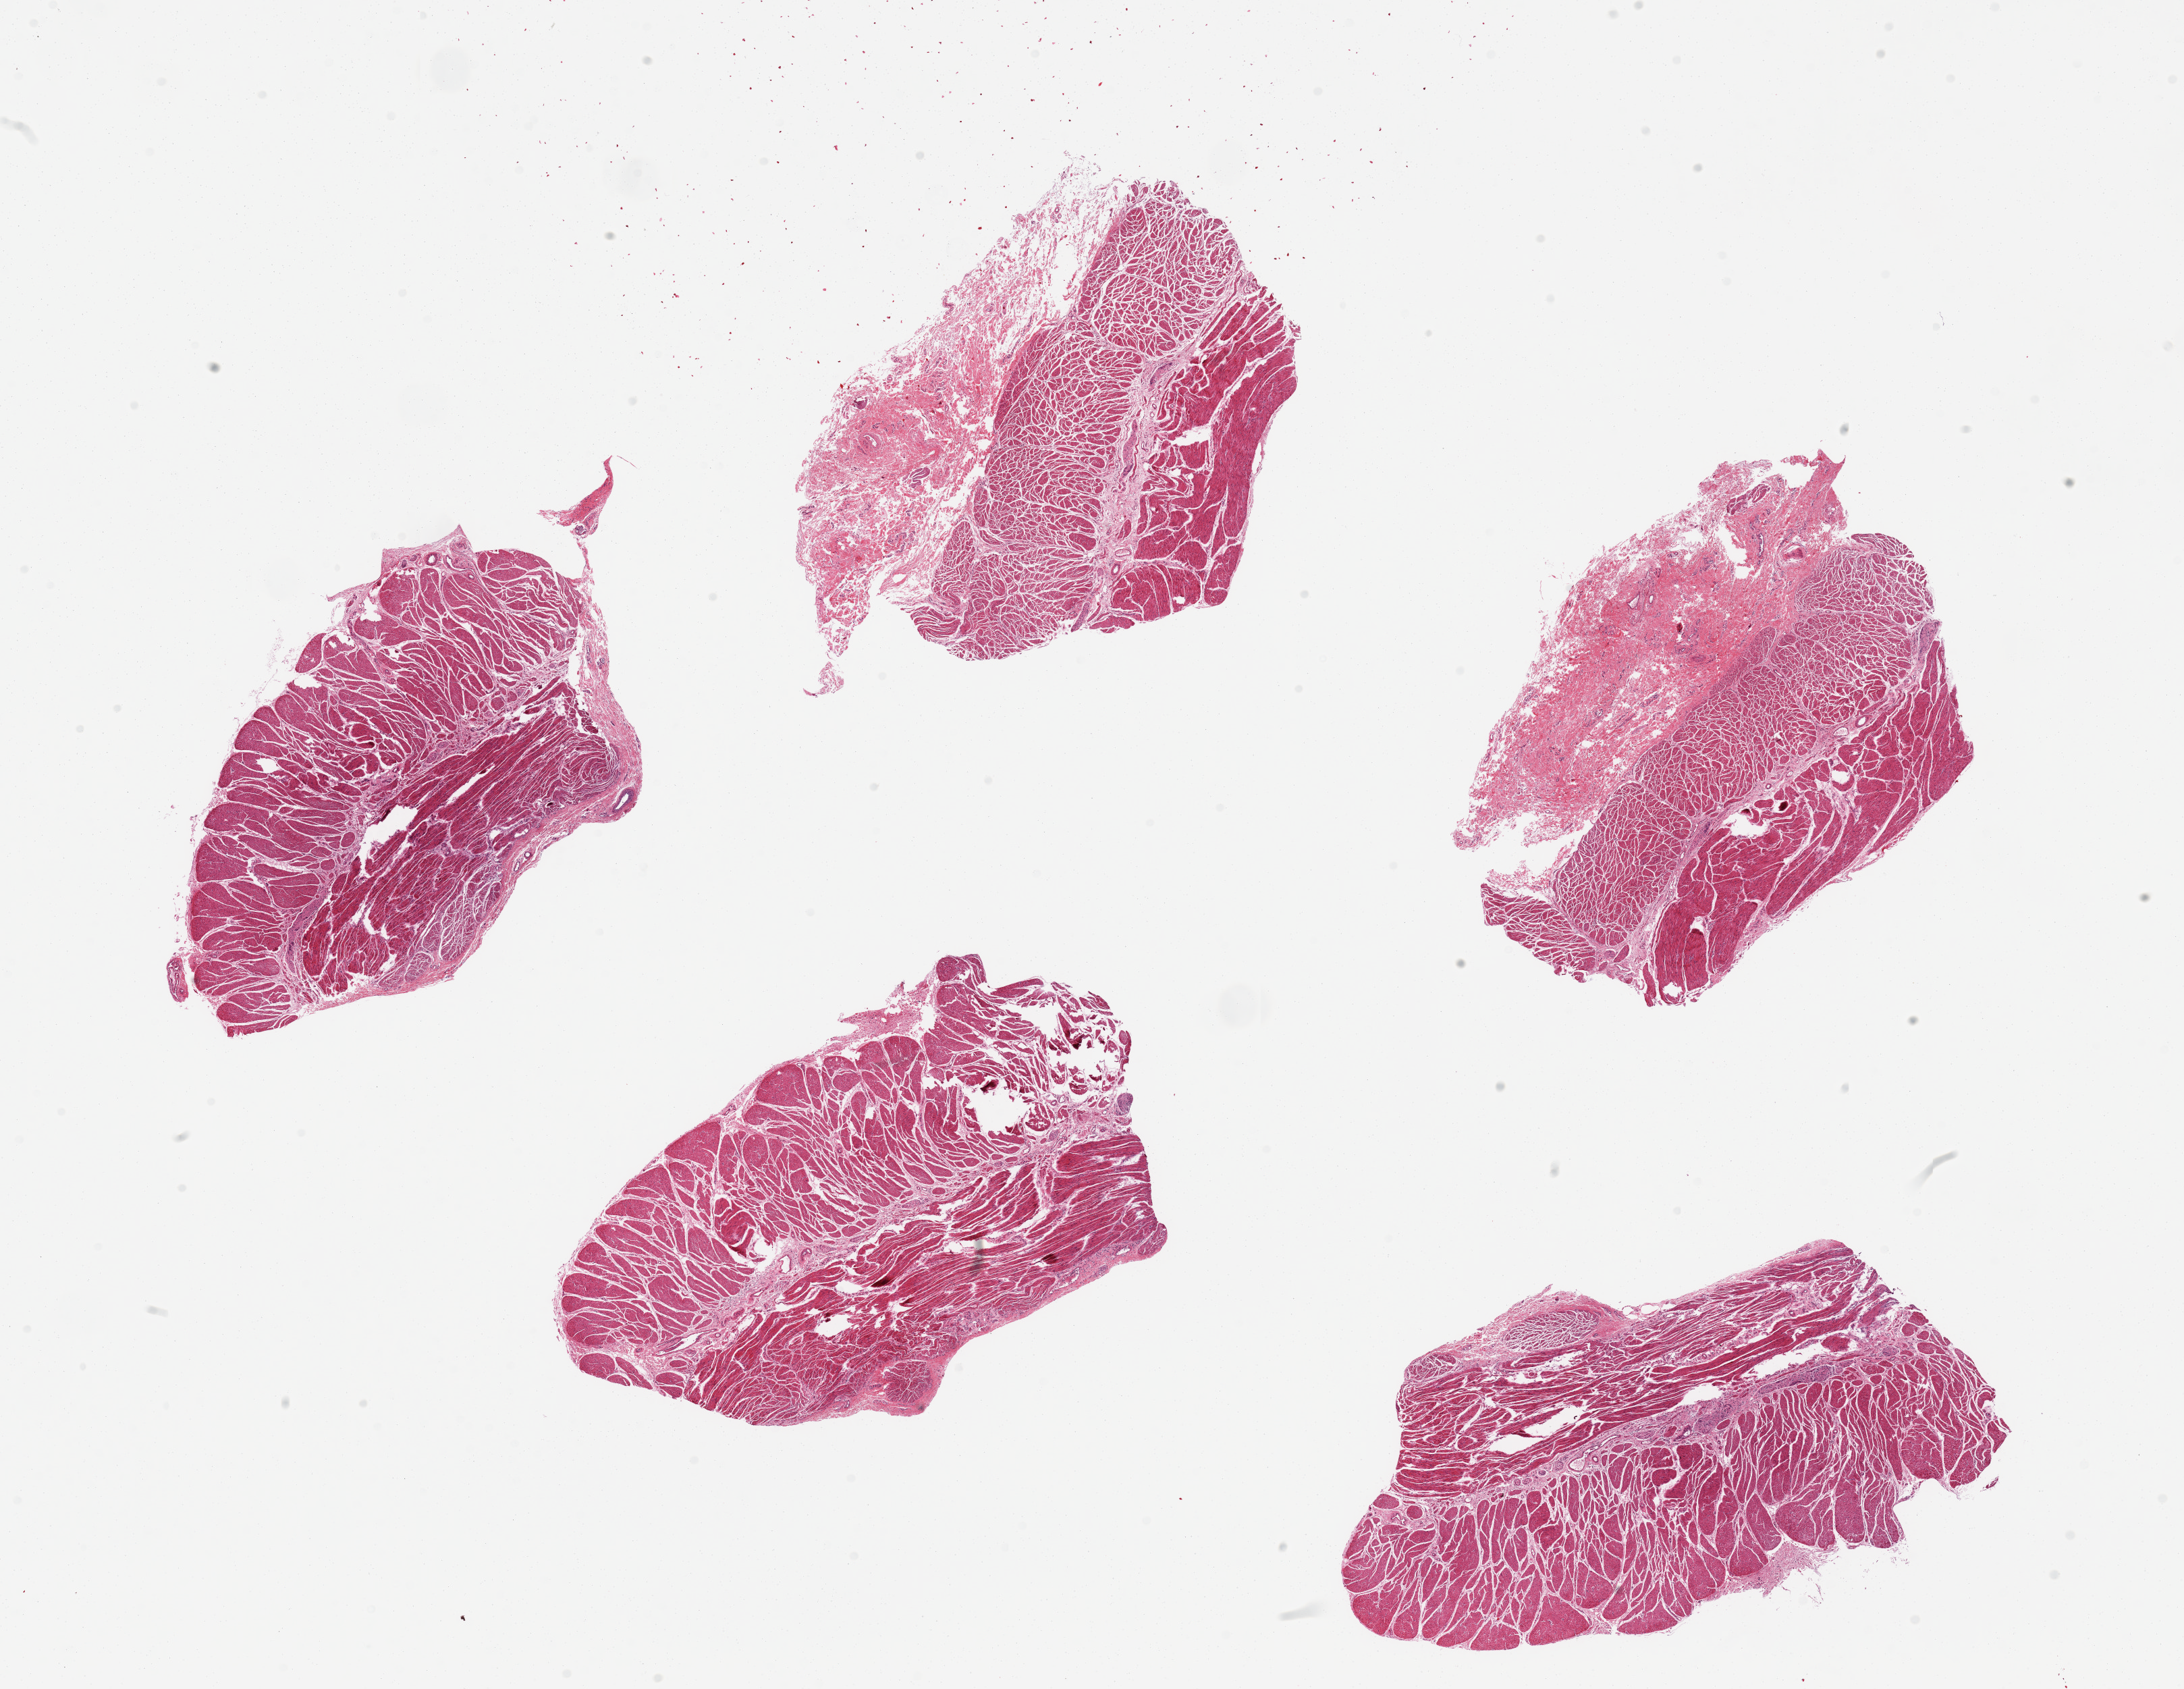
Haematoxylin and eosin whole-slide image — low-resolution overview of the scanned area, about 25.6 x 19.8 mm (from a 20x scan), PAXgene-fixed, paraffin-embedded tissue, target tissue: esophageal muscle, donor tissue sample. Male donor.
* pathologist's review note for this sample: 6 pieces, well trimmed but with few detached fragments of squamous epithelium